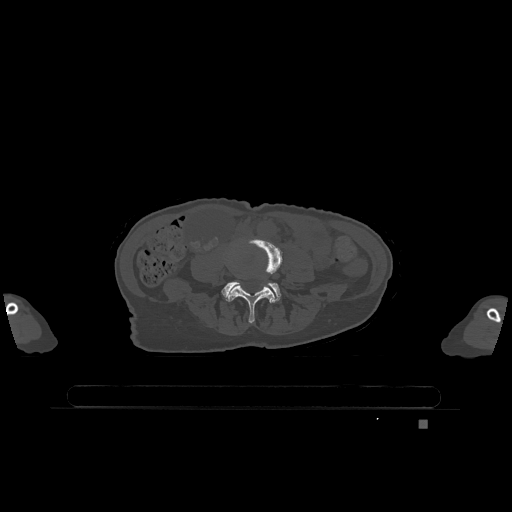
CT including the spine, one axial slice. Position 280 of 1317 along the scan axis. Bone window (W 1800 / L 400 HU). 0.5 mm slice thickness. 512 × 512 image matrix, field of view 500 × 500 mm. Patient: female, 74 years. Case-level facts recorded for this patient, not image findings: primary cancer: lung; vertebrae with lytic lesions (as recorded): T1, T4, T5, T6, L4, L5.
Structures marked on this image (semi-automatically segmented with operator editing):
- L4 vertebra: bounding box <226,238,283,323> (left, top, right, bottom; pixels)
- L5 vertebra: <222,281,281,302>